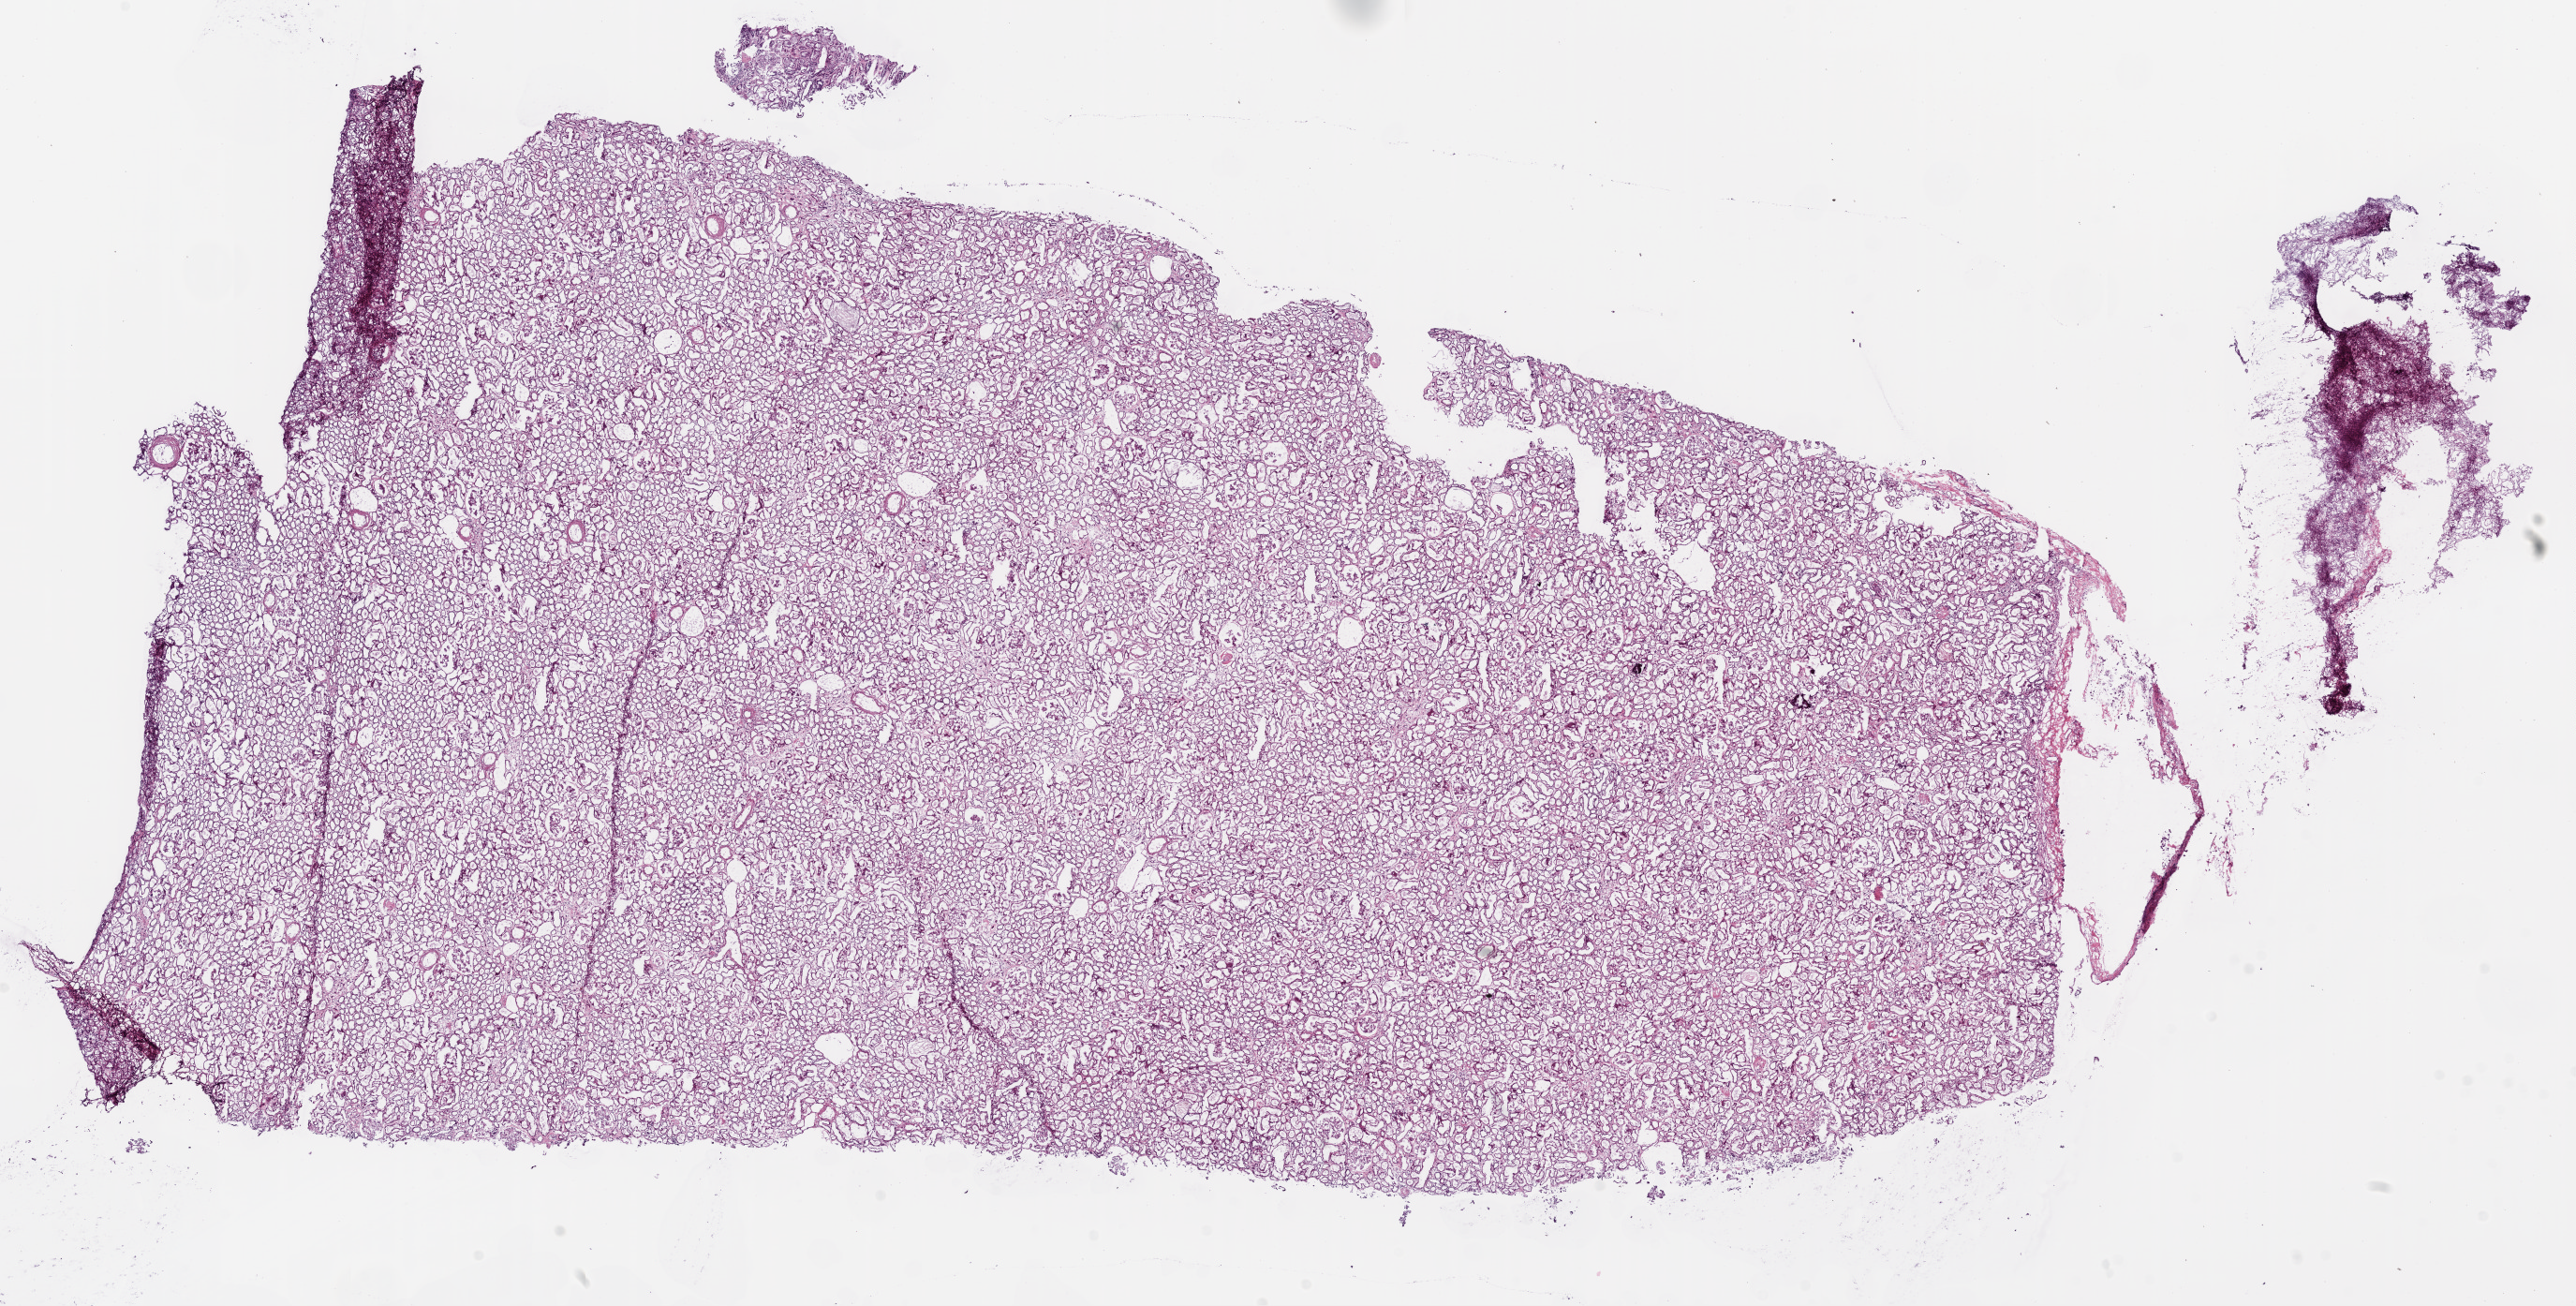
H&E-stained whole-slide image, shown as a low-resolution overview of the whole scanned area (about 22.1 x 11.2 mm, slide scanned at 20x); frozen section from the bottom of the tissue portion; sample: solid tissue normal (non-tumour tissue), kidney. Patient: female, age at initial diagnosis 76 years.
This section: solid tissue normal (non-tumour) sample from the same patient. Patient diagnosis: Clear cell adenocarcinoma, NOS.